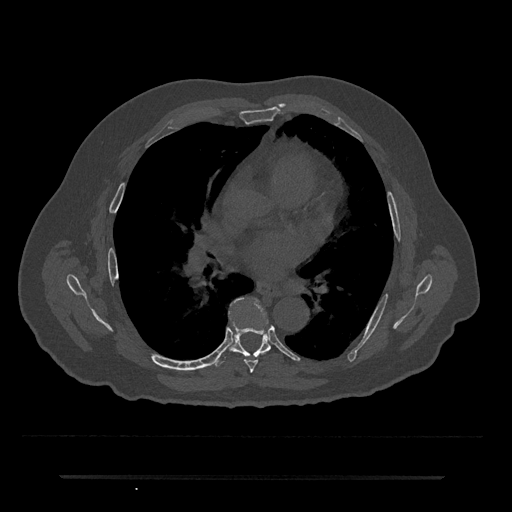
CT including the spine, one axial slice. Bone window (W 1800 / L 400 HU). 512 × 512 image matrix. Patient: male, 69 years. Case-level facts recorded for this patient, not image findings: primary cancer: prostate.
Structures marked on this image (semi-automatic segmentation, software-assisted and operator-edited):
- T6 vertebra: box from (x=237, y=298) to (x=261, y=373) px
- T7 vertebra: (x=214, y=321)–(x=271, y=366)